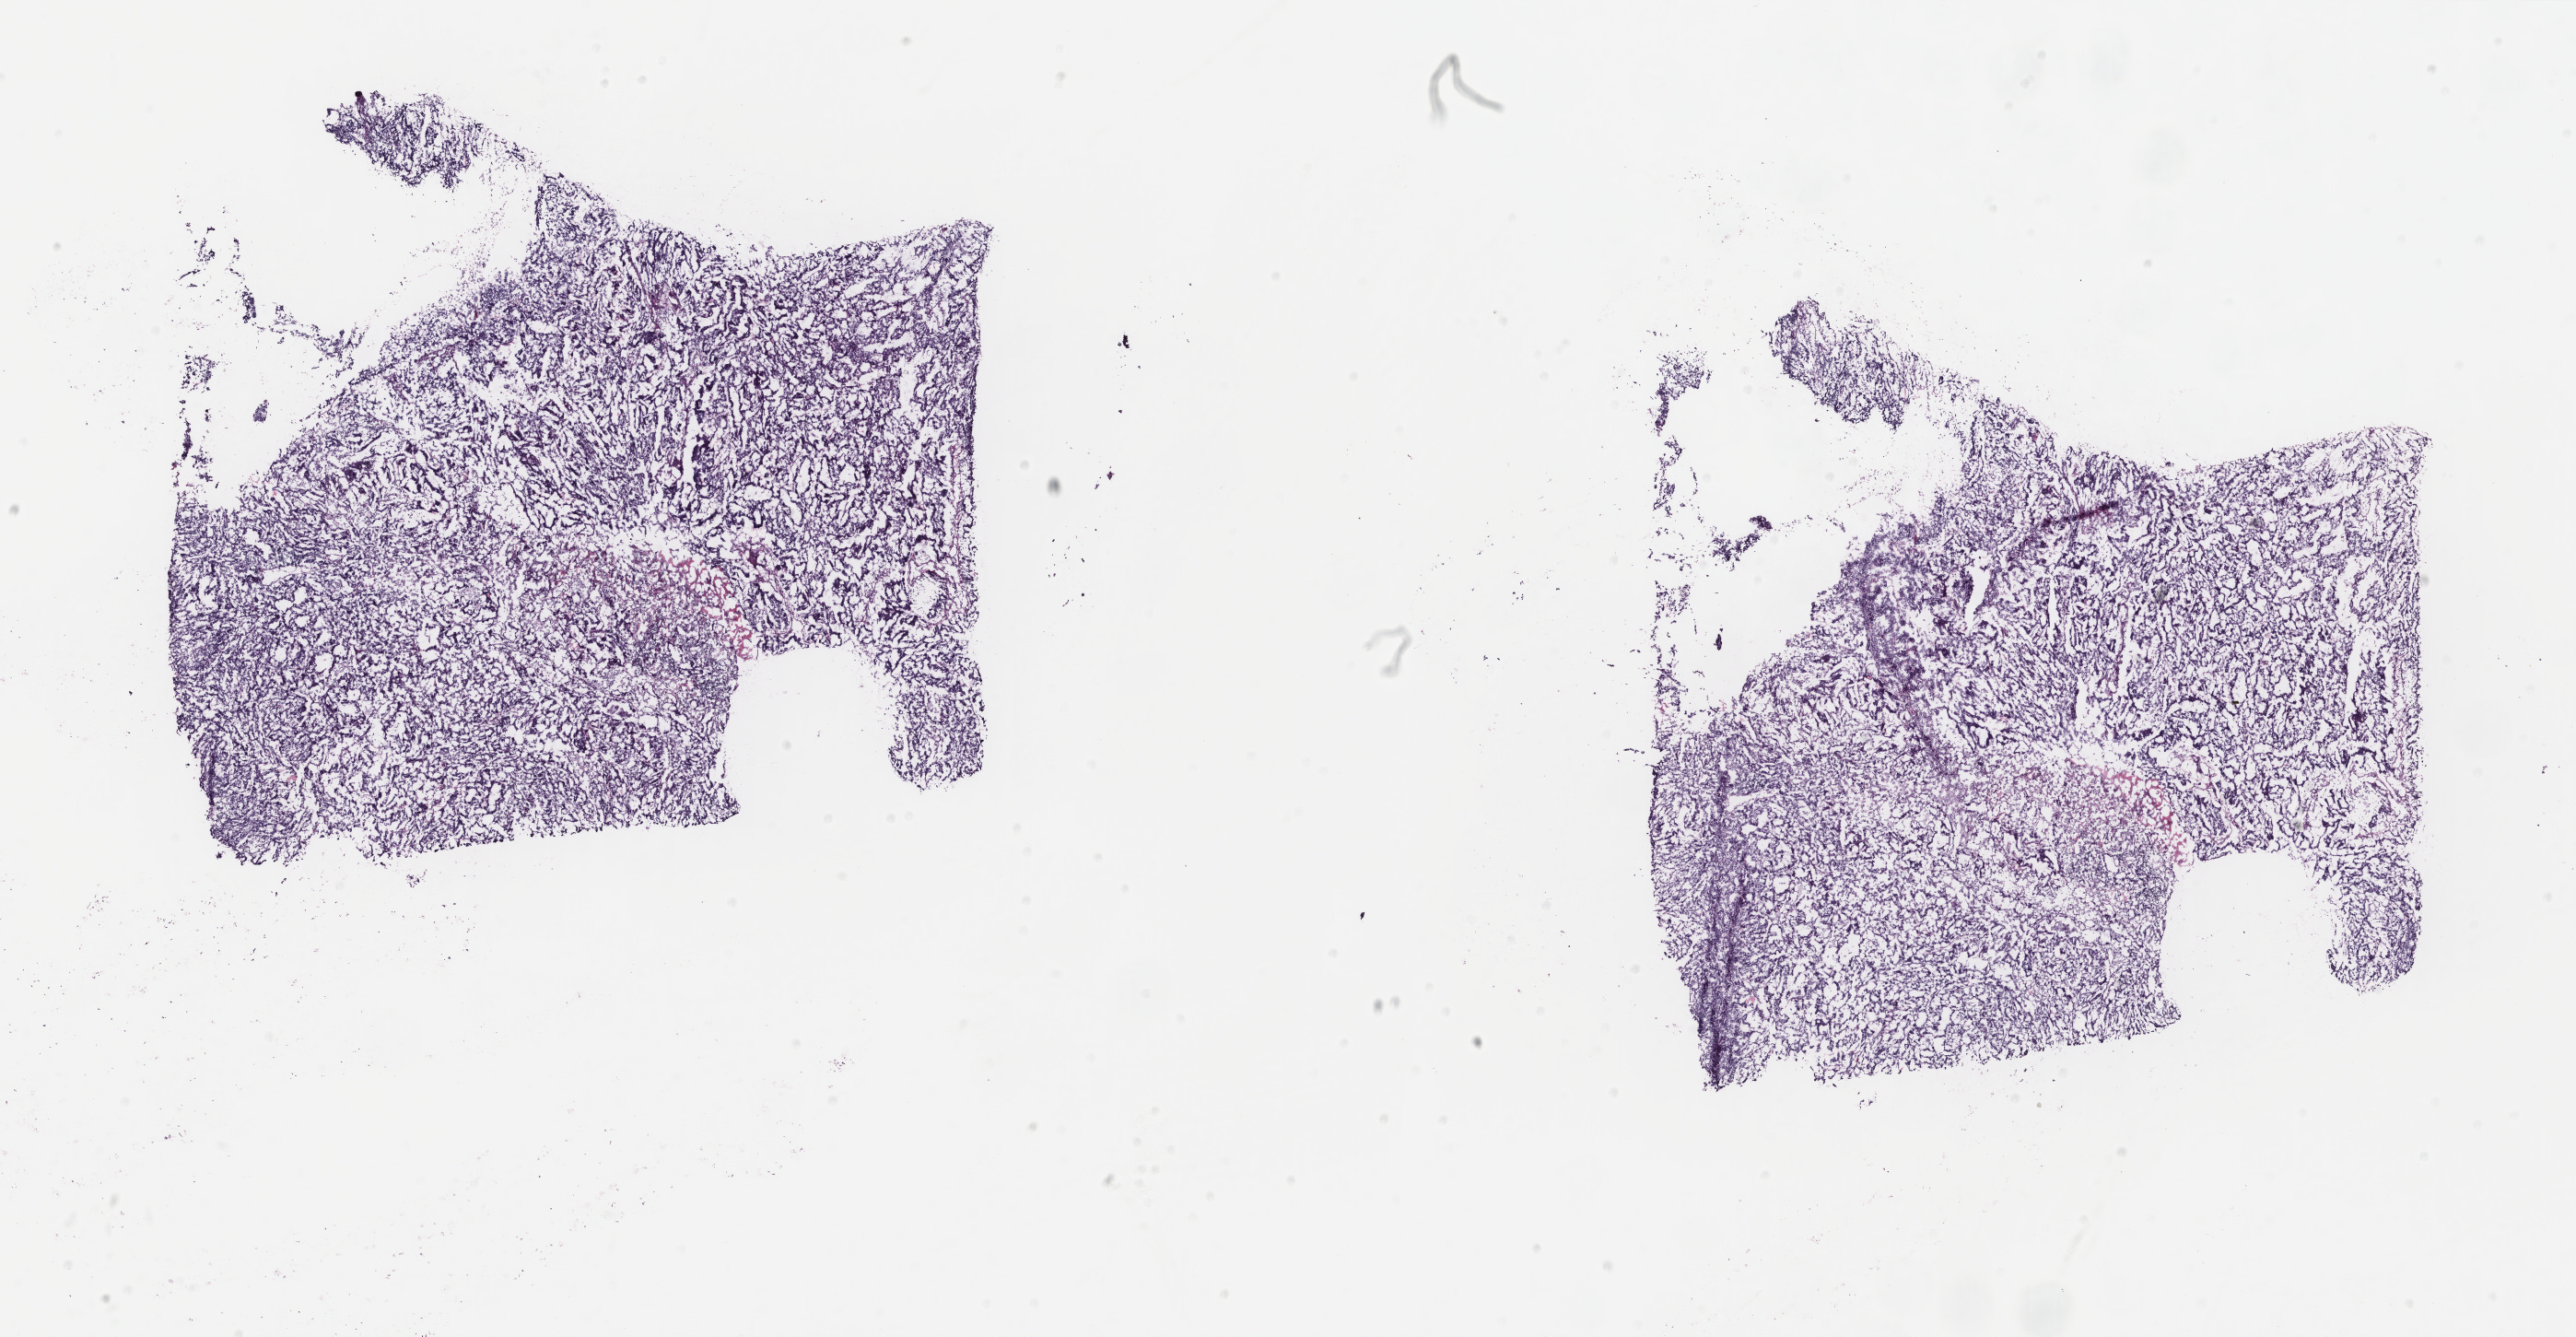
Whole-slide histology image, H&E, low-resolution overview of the scanned area, about 22.2 x 11.5 mm (from a 40x scan); frozen section from the top of the tissue portion; uterus, primary tumour sample. Patient: female, age at initial diagnosis 59 years. Histologic grade: G2 (moderately differentiated). Composition of this section per pathologist review: tumour cells 91%, tumour nuclei 90%, normal cells 0%, stromal cells 7%, necrosis 2%. Infiltration values recorded for this section: lymphocyte infiltration 8%, monocyte infiltration 2%, neutrophil infiltration 2%.
FIGO stage: IC. Histologic diagnosis: Endometrioid adenocarcinoma, NOS (endometrium).